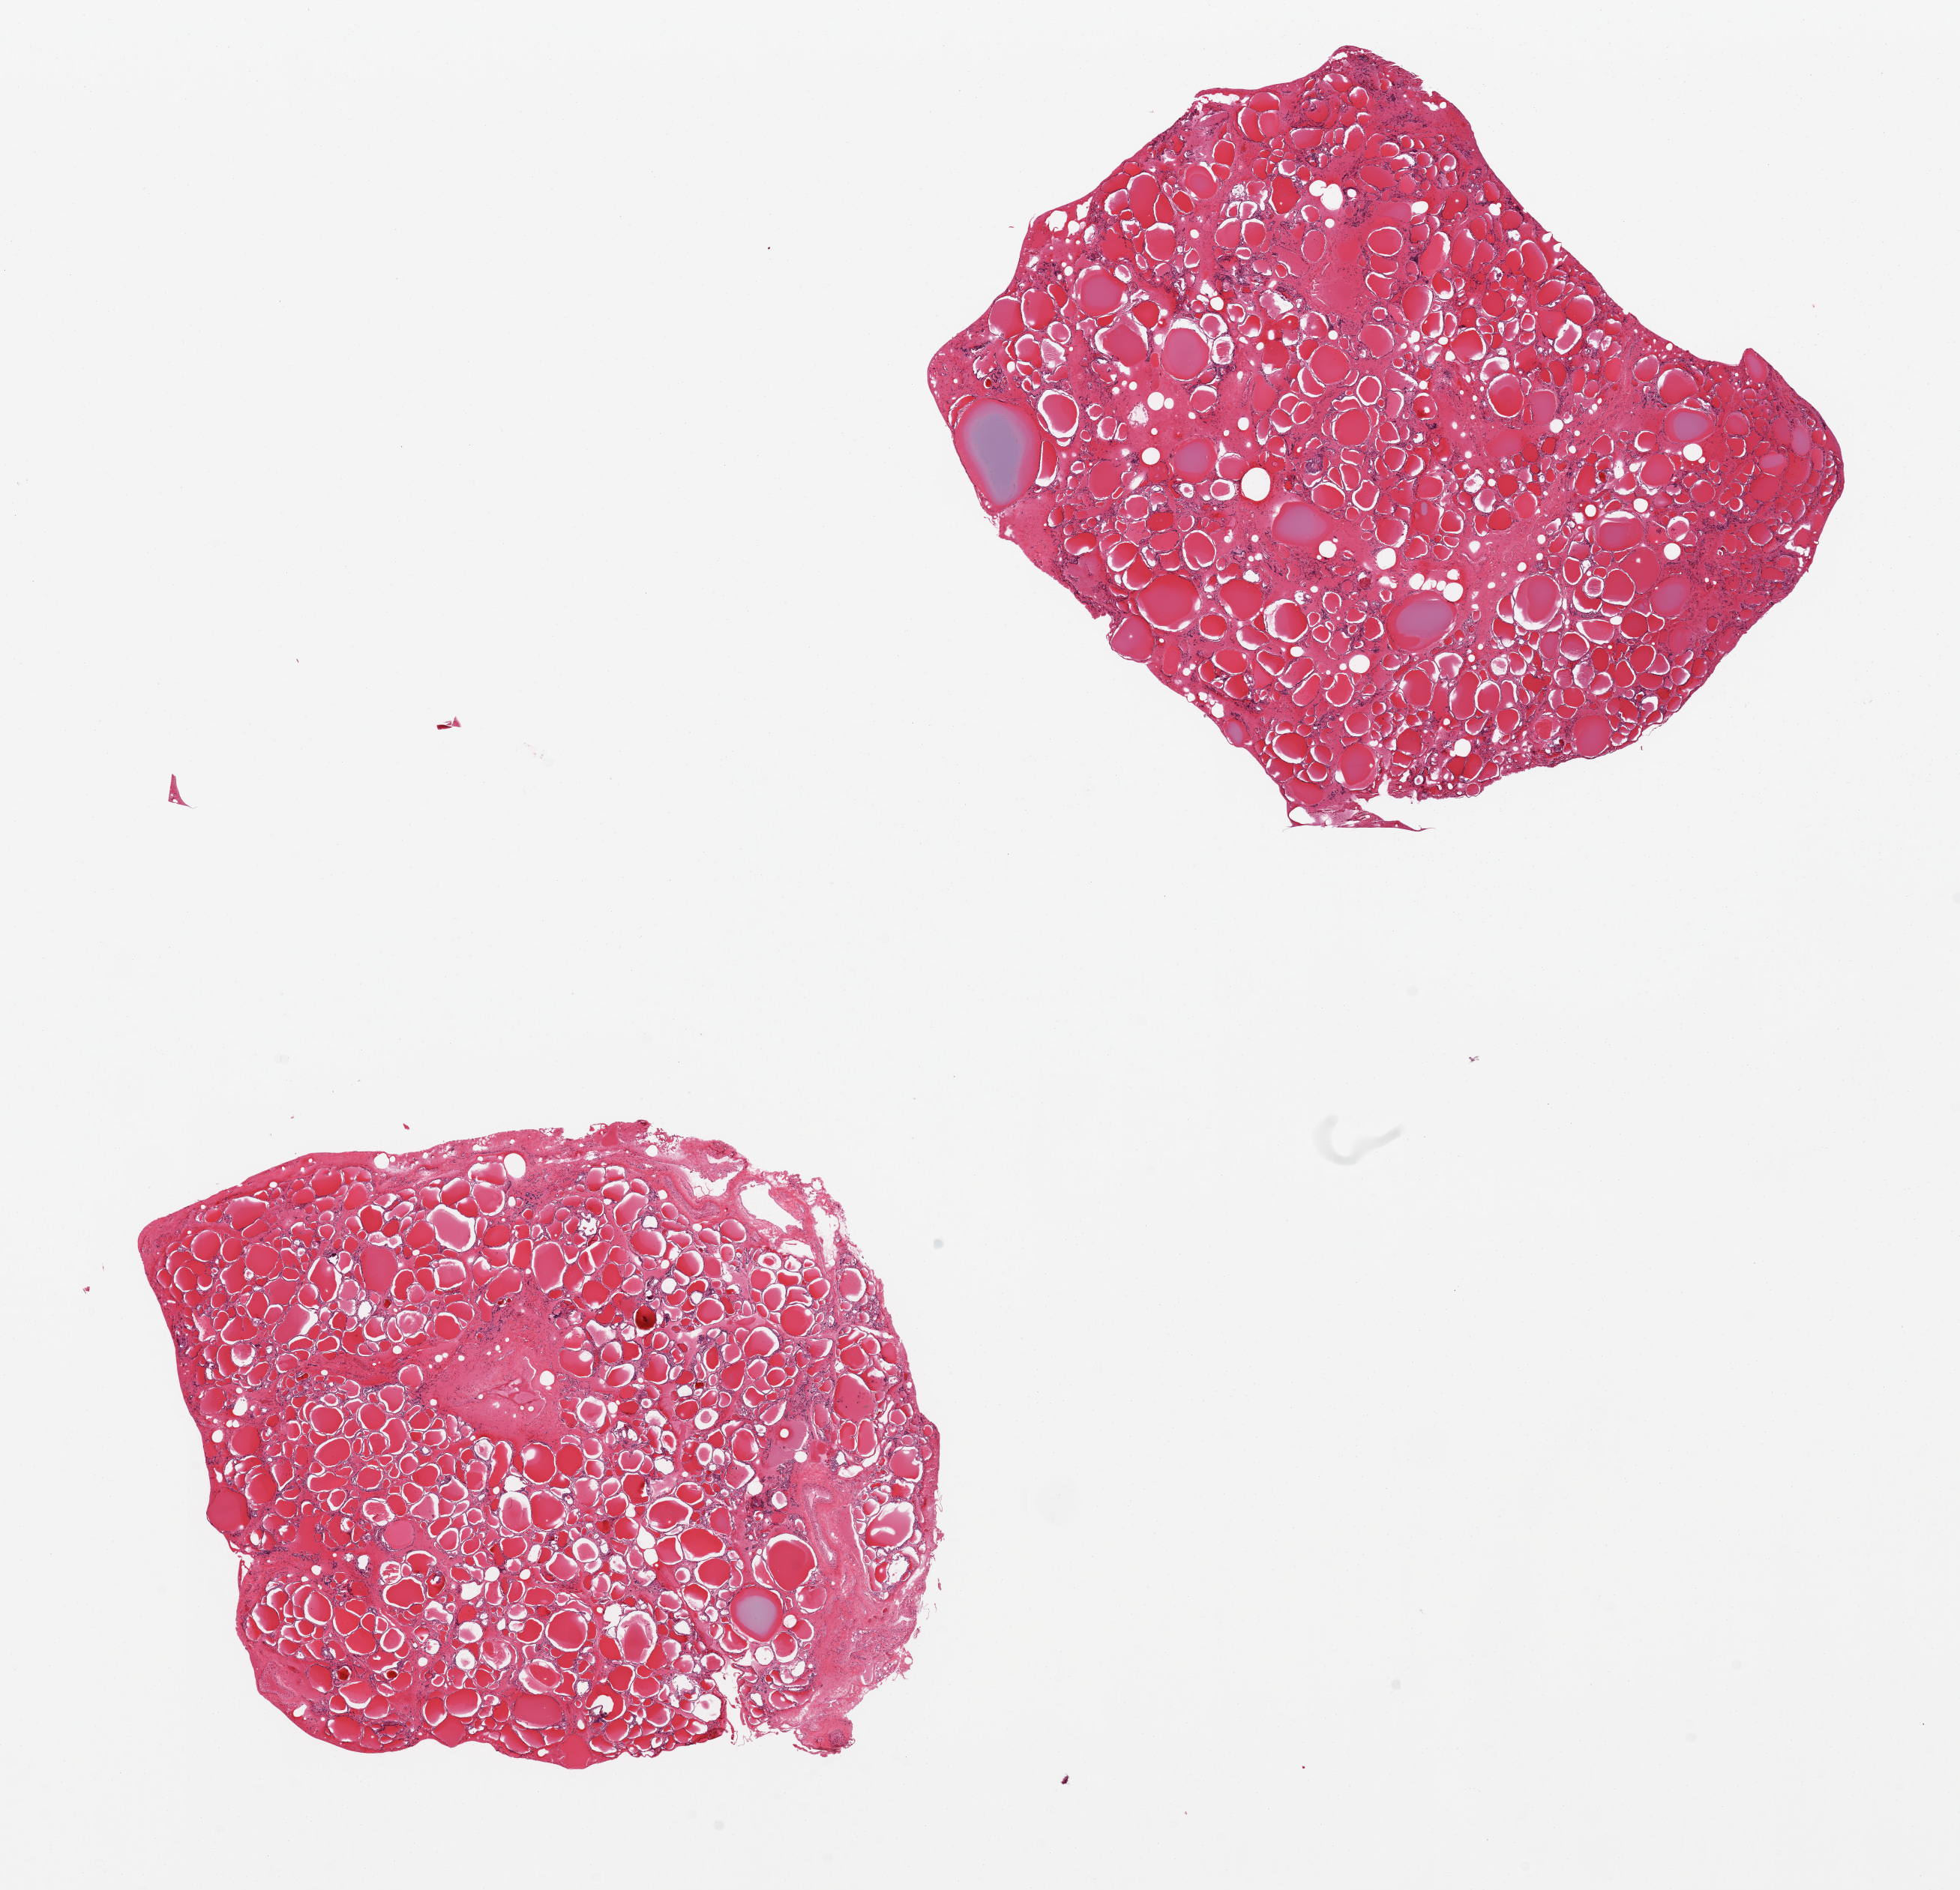
Hematoxylin and eosin (H&E) whole-slide image, brightfield — whole scanned area (about 20.7 x 19.9 mm) shown as a low-resolution overview; PAXgene-fixed, paraffin-embedded tissue; target tissue: thyroid; tissue donor sample. Donor sex: male.
Pathologist's review note for this sample: 2 pieces; multiple colloid cysts.